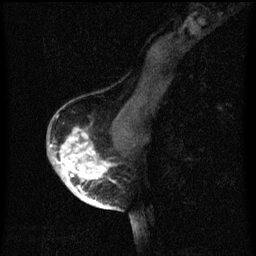
Breast MRI (dynamic contrast-enhanced), one sagittal slice; slice 37 of 60 in the series (ordered by position); dynamic contrast-enhanced series, image 2 of 3 at this slice position (ordered by acquisition); 1.5 T; TE 4.2 ms, TR 8 ms; 2 mm slice thickness; 256 × 256 image matrix, field of view 180 × 180 mm. Female patient, age 56 years.
Annotated regions visible in this slice (semi-automatically segmented with operator editing):
- analysis volume of interest (the breast-tissue region the enhancement analysis was run in; not a lesion): bounding box (x1, y1, x2, y2) in pixels: (54, 122, 120, 199)
- tumour enhancement mask (voxels above the 70 % enhancement threshold inside the analysis volume of interest): (55, 128, 113, 199)